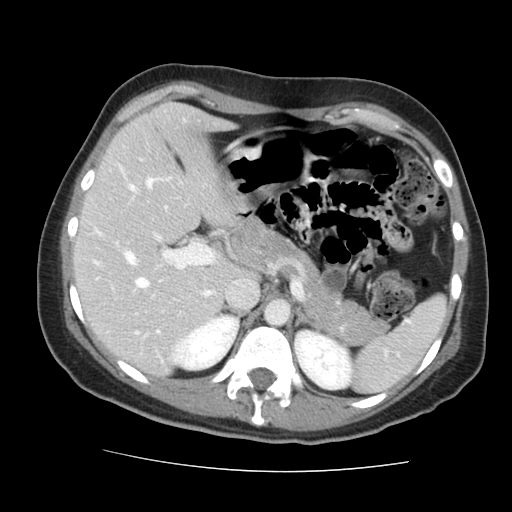
Contrast-enhanced abdominal CT, one axial slice. Slice 95 of 144 in the series (ordered by position). 120 kVp. Intravenous contrast given. Soft-tissue window (W 400 / L 40 HU). 2.5 mm slice thickness. 512 × 512 image matrix, field of view 333 × 333 mm. Female patient, age 46 years. Case-level facts recorded for this patient, not image findings: diagnosis: colorectal cancer liver metastases, imaged before liver resection; multiple liver metastases: no; largest metastasis: 2.8 cm.
Structures marked on this image (expert manual segmentation):
- hepatic veins: bounding box <119,166,211,295> (left, top, right, bottom; pixels)
- liver: <76,105,232,374>
- planned liver remnant (the part of the liver to remain after resection): <76,105,232,374>
- portal vein (with intrahepatic branches): <97,232,216,333>